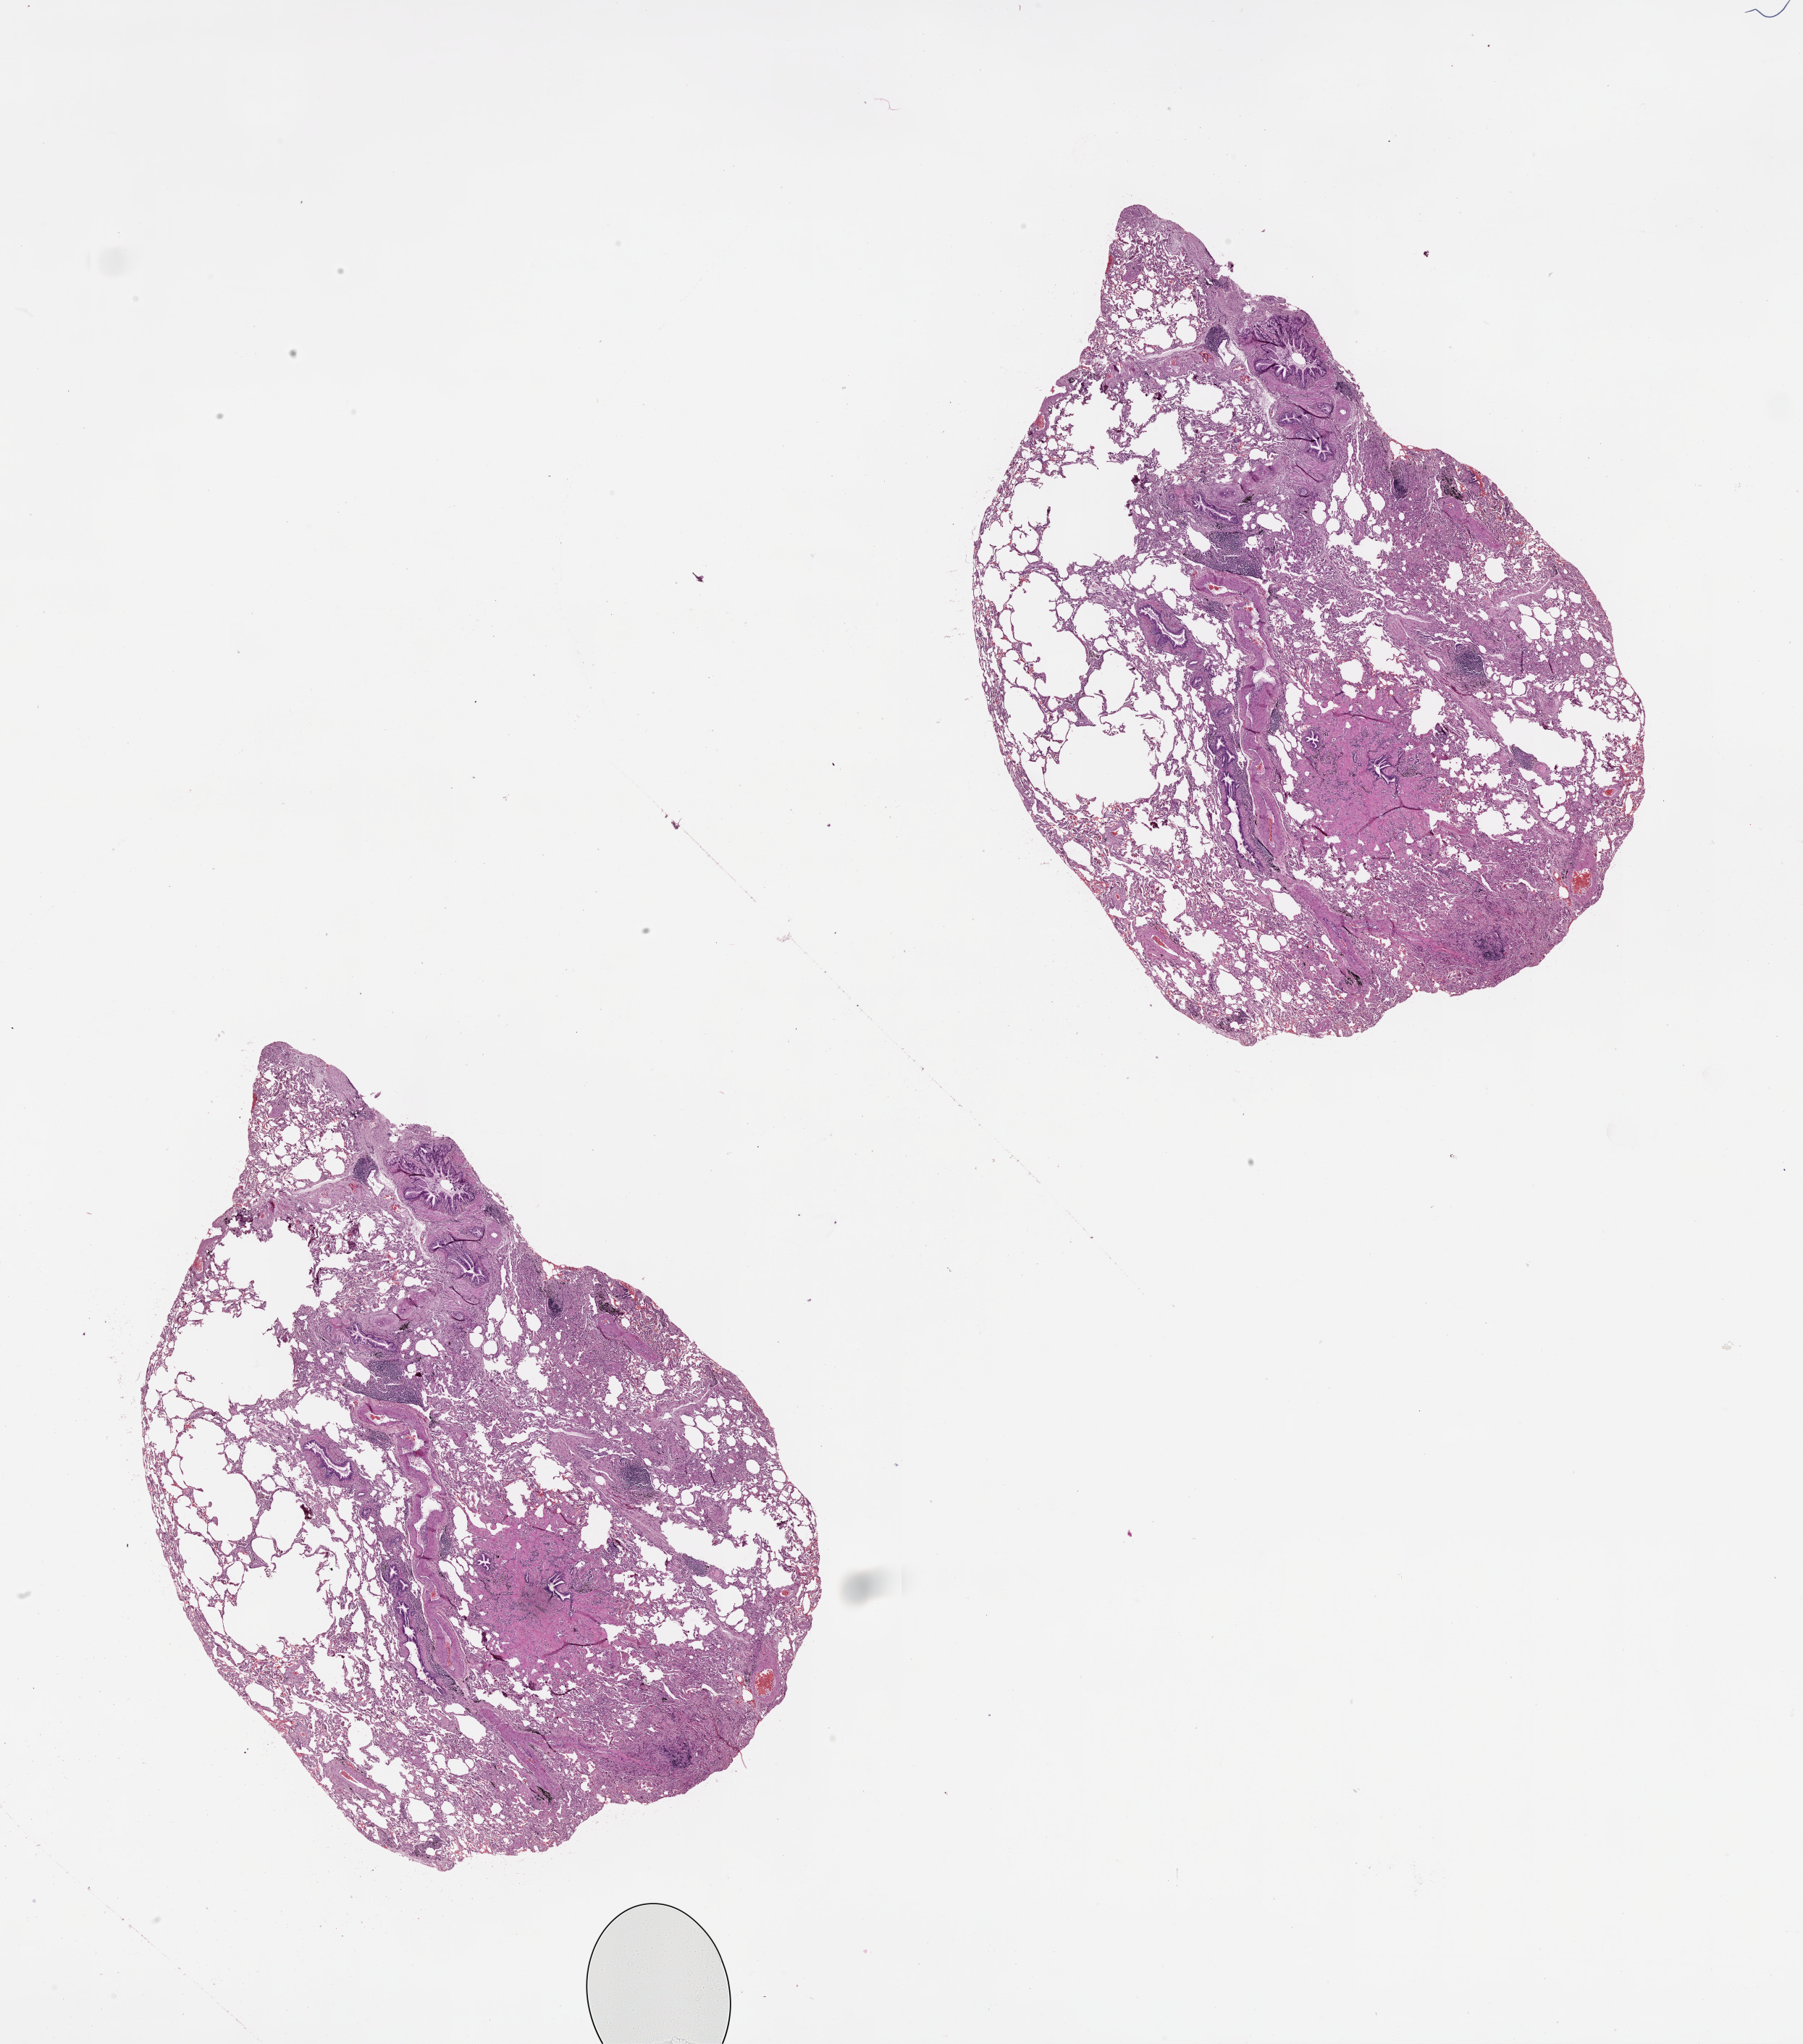
Digitized Hematoxylin and eosin (H&E) stained tissue section (whole slide), low-resolution overview of the scanned area, about 20.0 x 22.7 mm, normal (non-tumour) tissue sample, lung. 60-year-old female patient.
This section: normal (non-tumour) tissue from the same patient. Patient diagnosis (cohort enrolment): squamous cell carcinoma (lung).